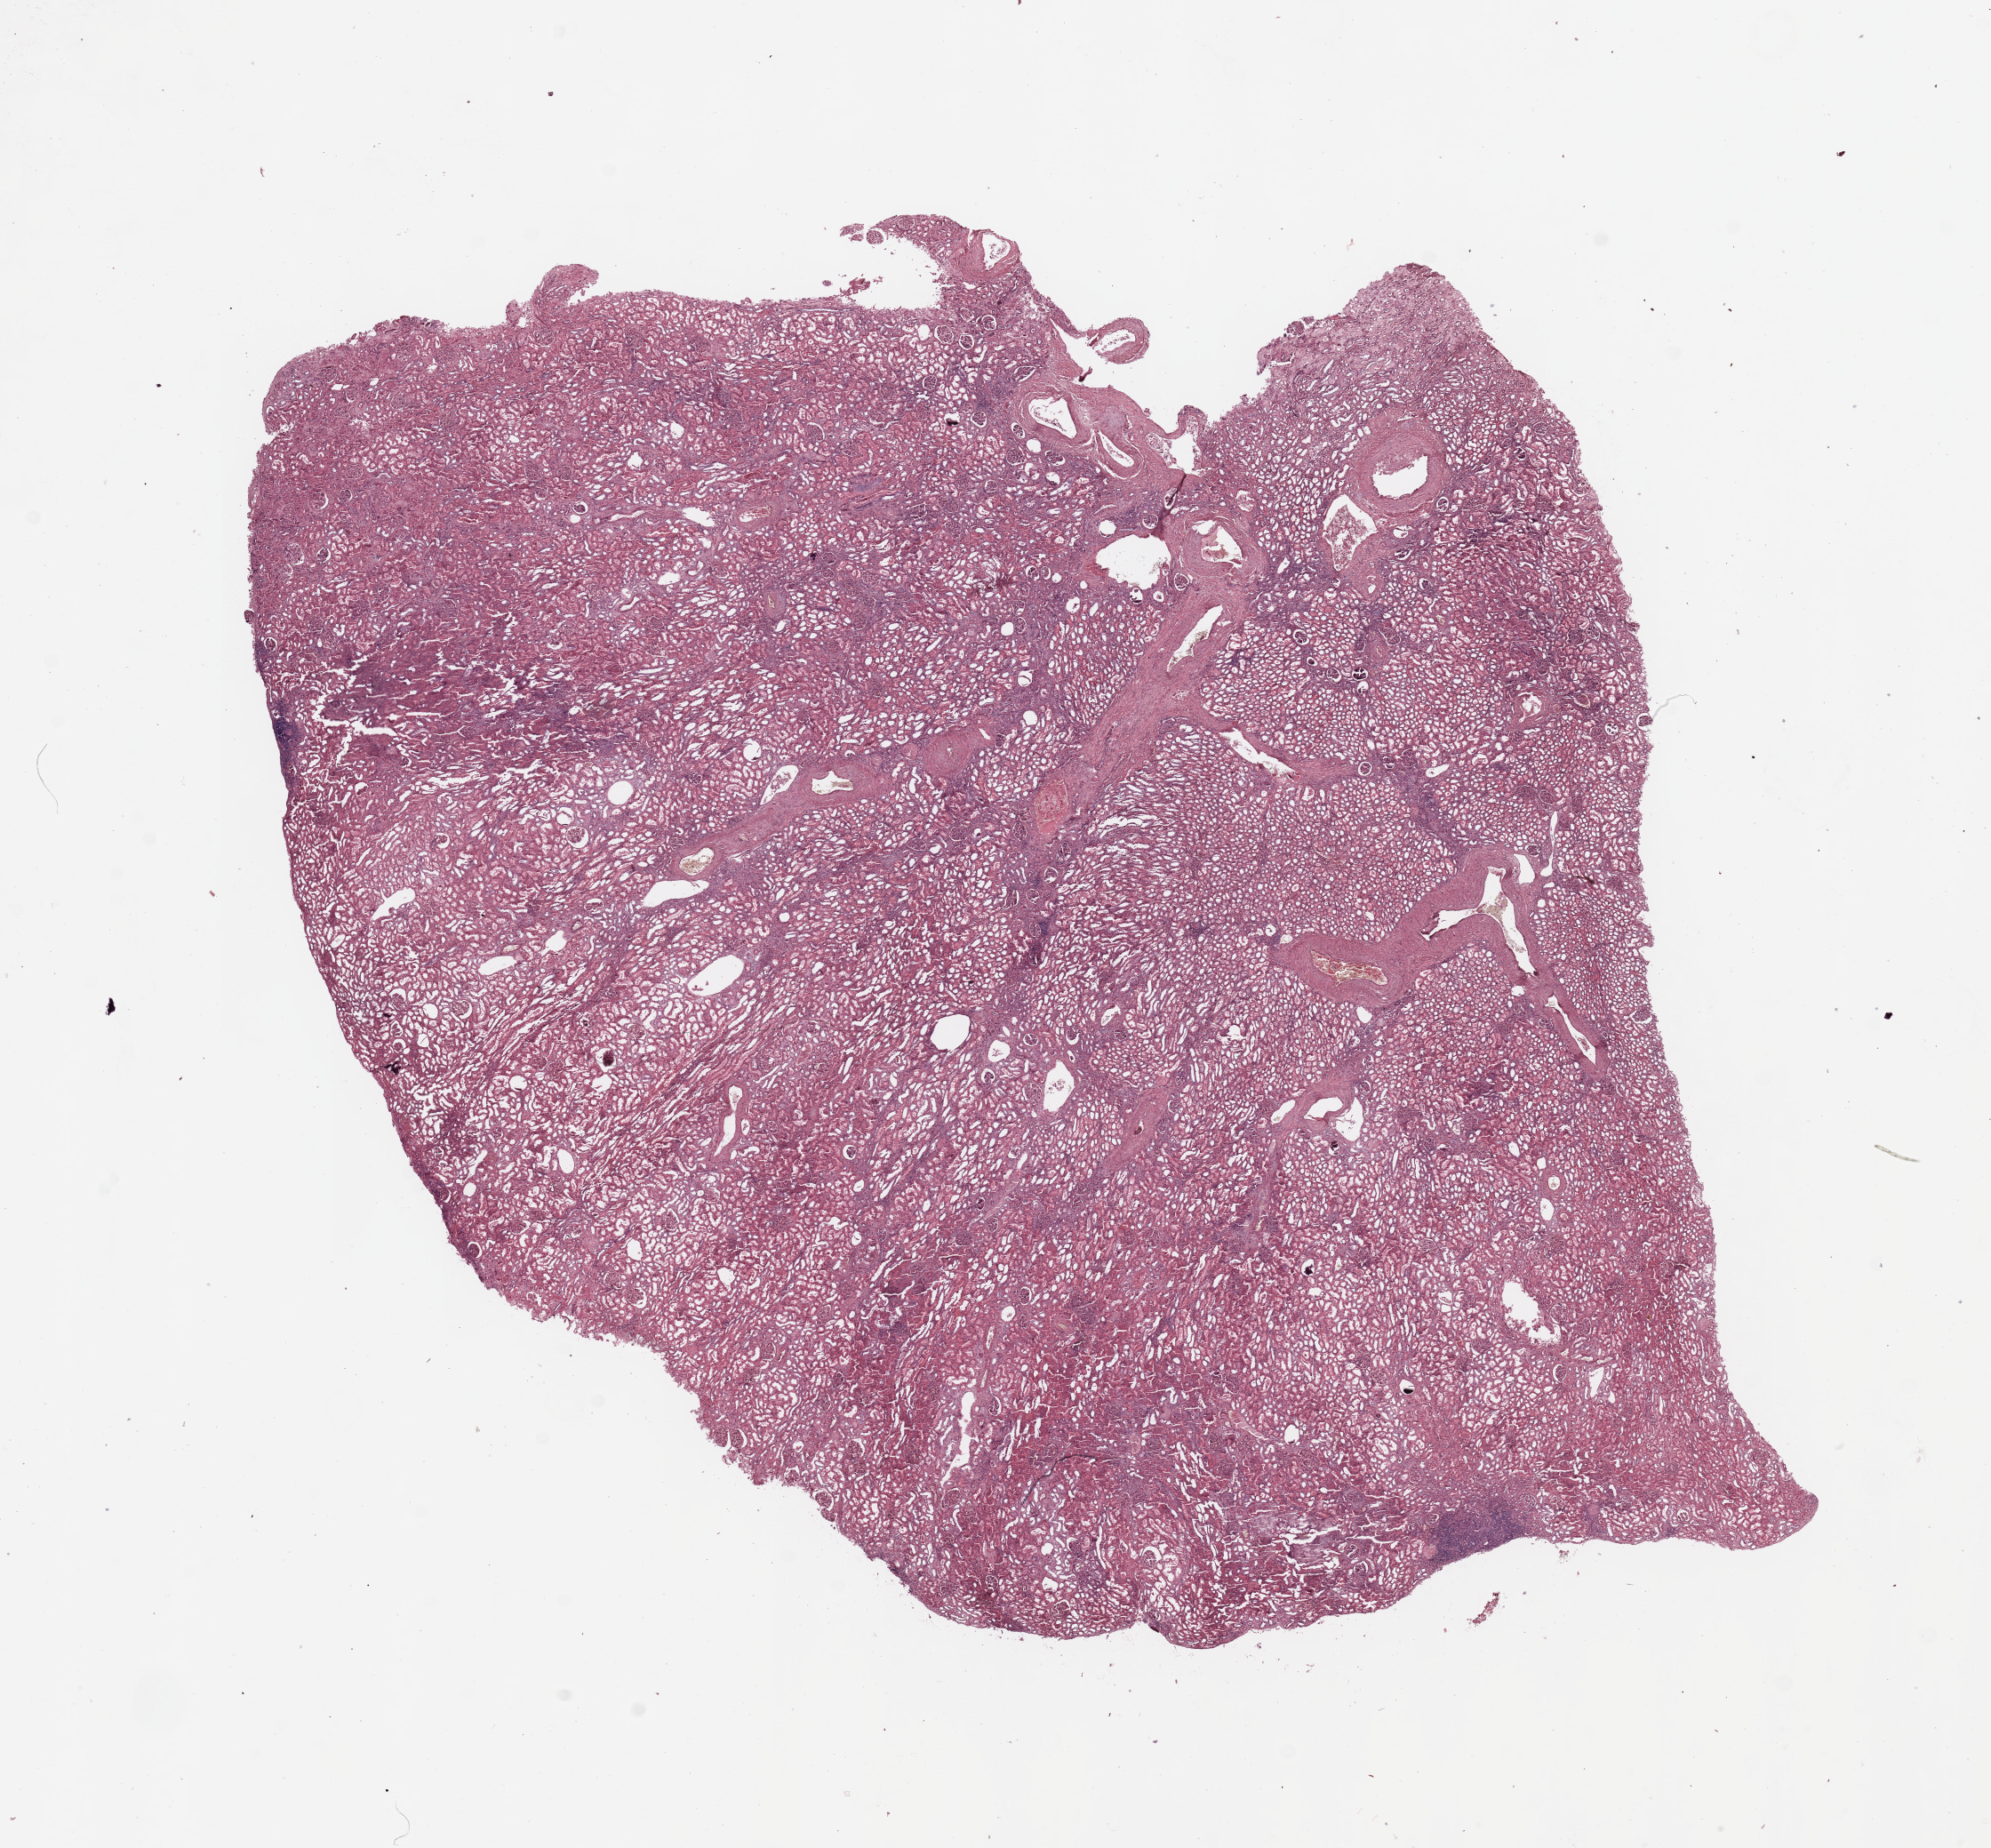
Whole-slide histology image, Hematoxylin and eosin (H&E) stained — low-resolution overview of the scanned area, about 17.7 x 16.4 mm (slide scanned at 20x). Patient: male, age 64 years.
• patient diagnosis (cohort enrolment): sarcoma (site not recorded at cohort level)